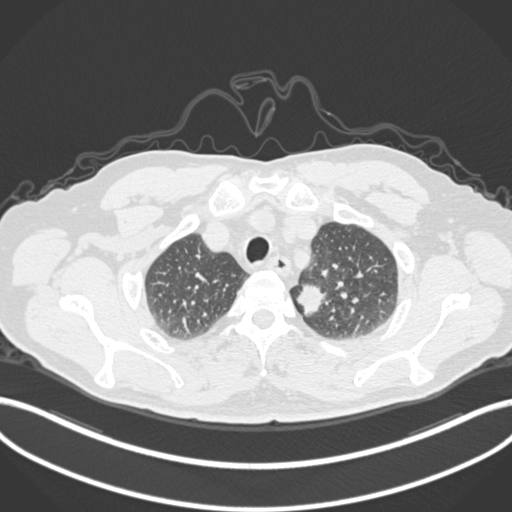
Chest CT, one axial slice. Slice 272 of 306 in the series (ordered by position). Reconstruction kernel B30f. 120 kVp. Lung window (W 1500 / L -600 HU). 1 mm slice thickness. 512 × 512 image matrix, field of view 400 × 400 mm. Male patient, age 64 years. From the clinical record (not read from this slice): clinical TNM (as recorded): T1c N0 M0.
Annotated regions visible in this slice (rectangle marked by the reading radiologist):
- lung tumour (recorded histology: adenocarcinoma): bounding box [x1, y1, x2, y2] px = [294, 280, 329, 319]